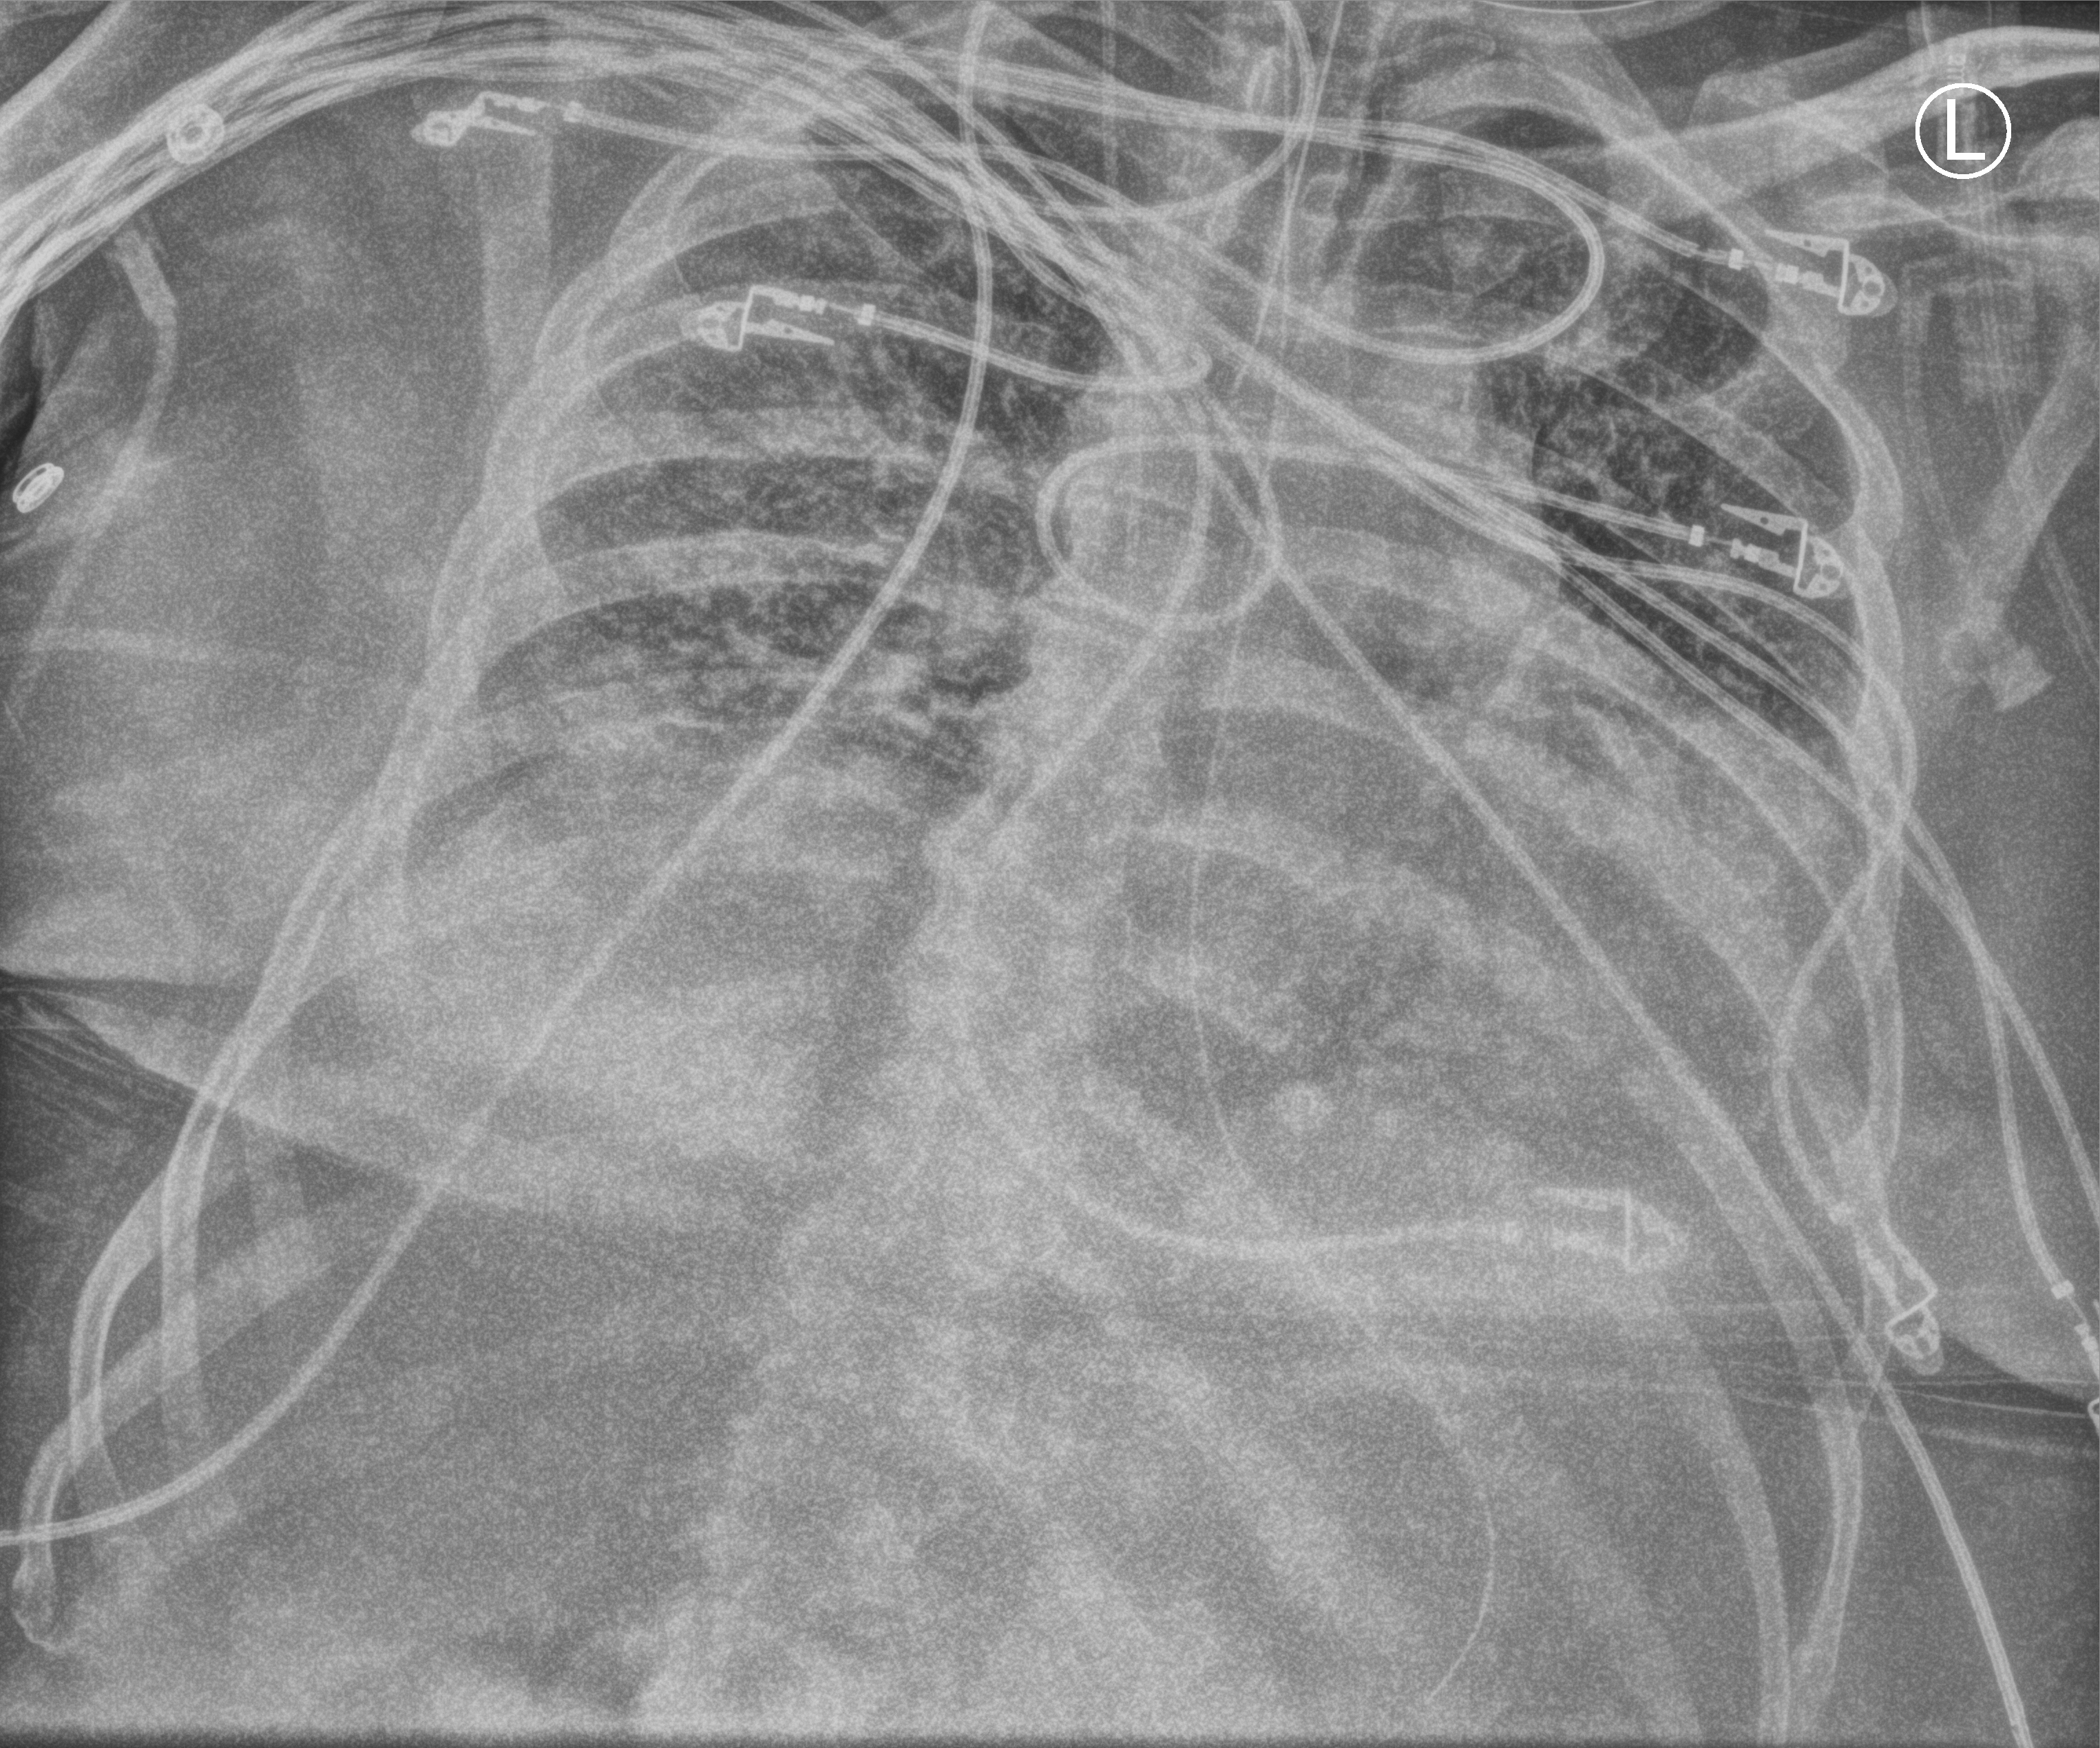
Portable chest radiograph; anteroposterior (AP) projection. Patient hospitalised with COVID-19; male, aged 60–74 years.
Hospital-stay facts (about this admission, not read from this image; timing relative to this image not recorded): admitted to intensive care during this hospital stay: yes.